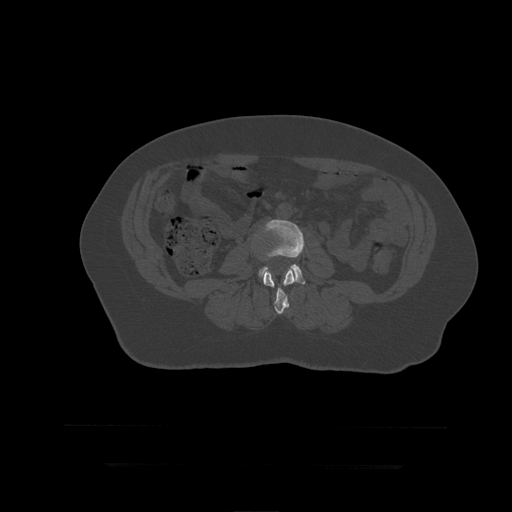
CT including the spine, one axial slice. Position 111 of 399 along the scan axis. Reconstruction kernel STANDARD. Bone window (W 1800 / L 400 HU). 512 × 512 image matrix, field of view 450 × 450 mm. Patient age 41 years. Case-level facts recorded for this patient, not image findings: primary cancer: breast.
Annotated regions visible in this slice (semi-automatically segmented with operator editing):
- L3 vertebra: bounding box <263,268,296,314> (left, top, right, bottom; pixels)
- L4 vertebra: <259,220,306,285>